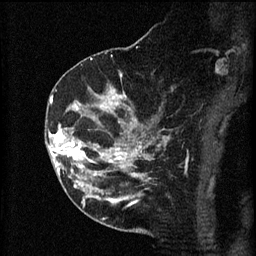
Breast MRI (dynamic contrast-enhanced), one sagittal slice; position 34 of 60 along the scan axis; 3 images stored at this slice position (order not interpretable as contrast timing); 1.5 T; TE 4.2 ms, TR 8.2 ms; 2 mm slice thickness; 256 × 256 image matrix, field of view 180 × 180 mm. Female patient, age 49 years.
Annotated regions visible in this slice (semi-automatic segmentation, software-assisted and operator-edited):
- analysis volume of interest (the breast-tissue region the enhancement analysis was run in; not a lesion): bounding box (x1, y1, x2, y2) in pixels: (45, 126, 105, 177)
- tumour enhancement mask (voxels above the 70 % enhancement threshold inside the analysis volume of interest): (49, 126, 98, 177)